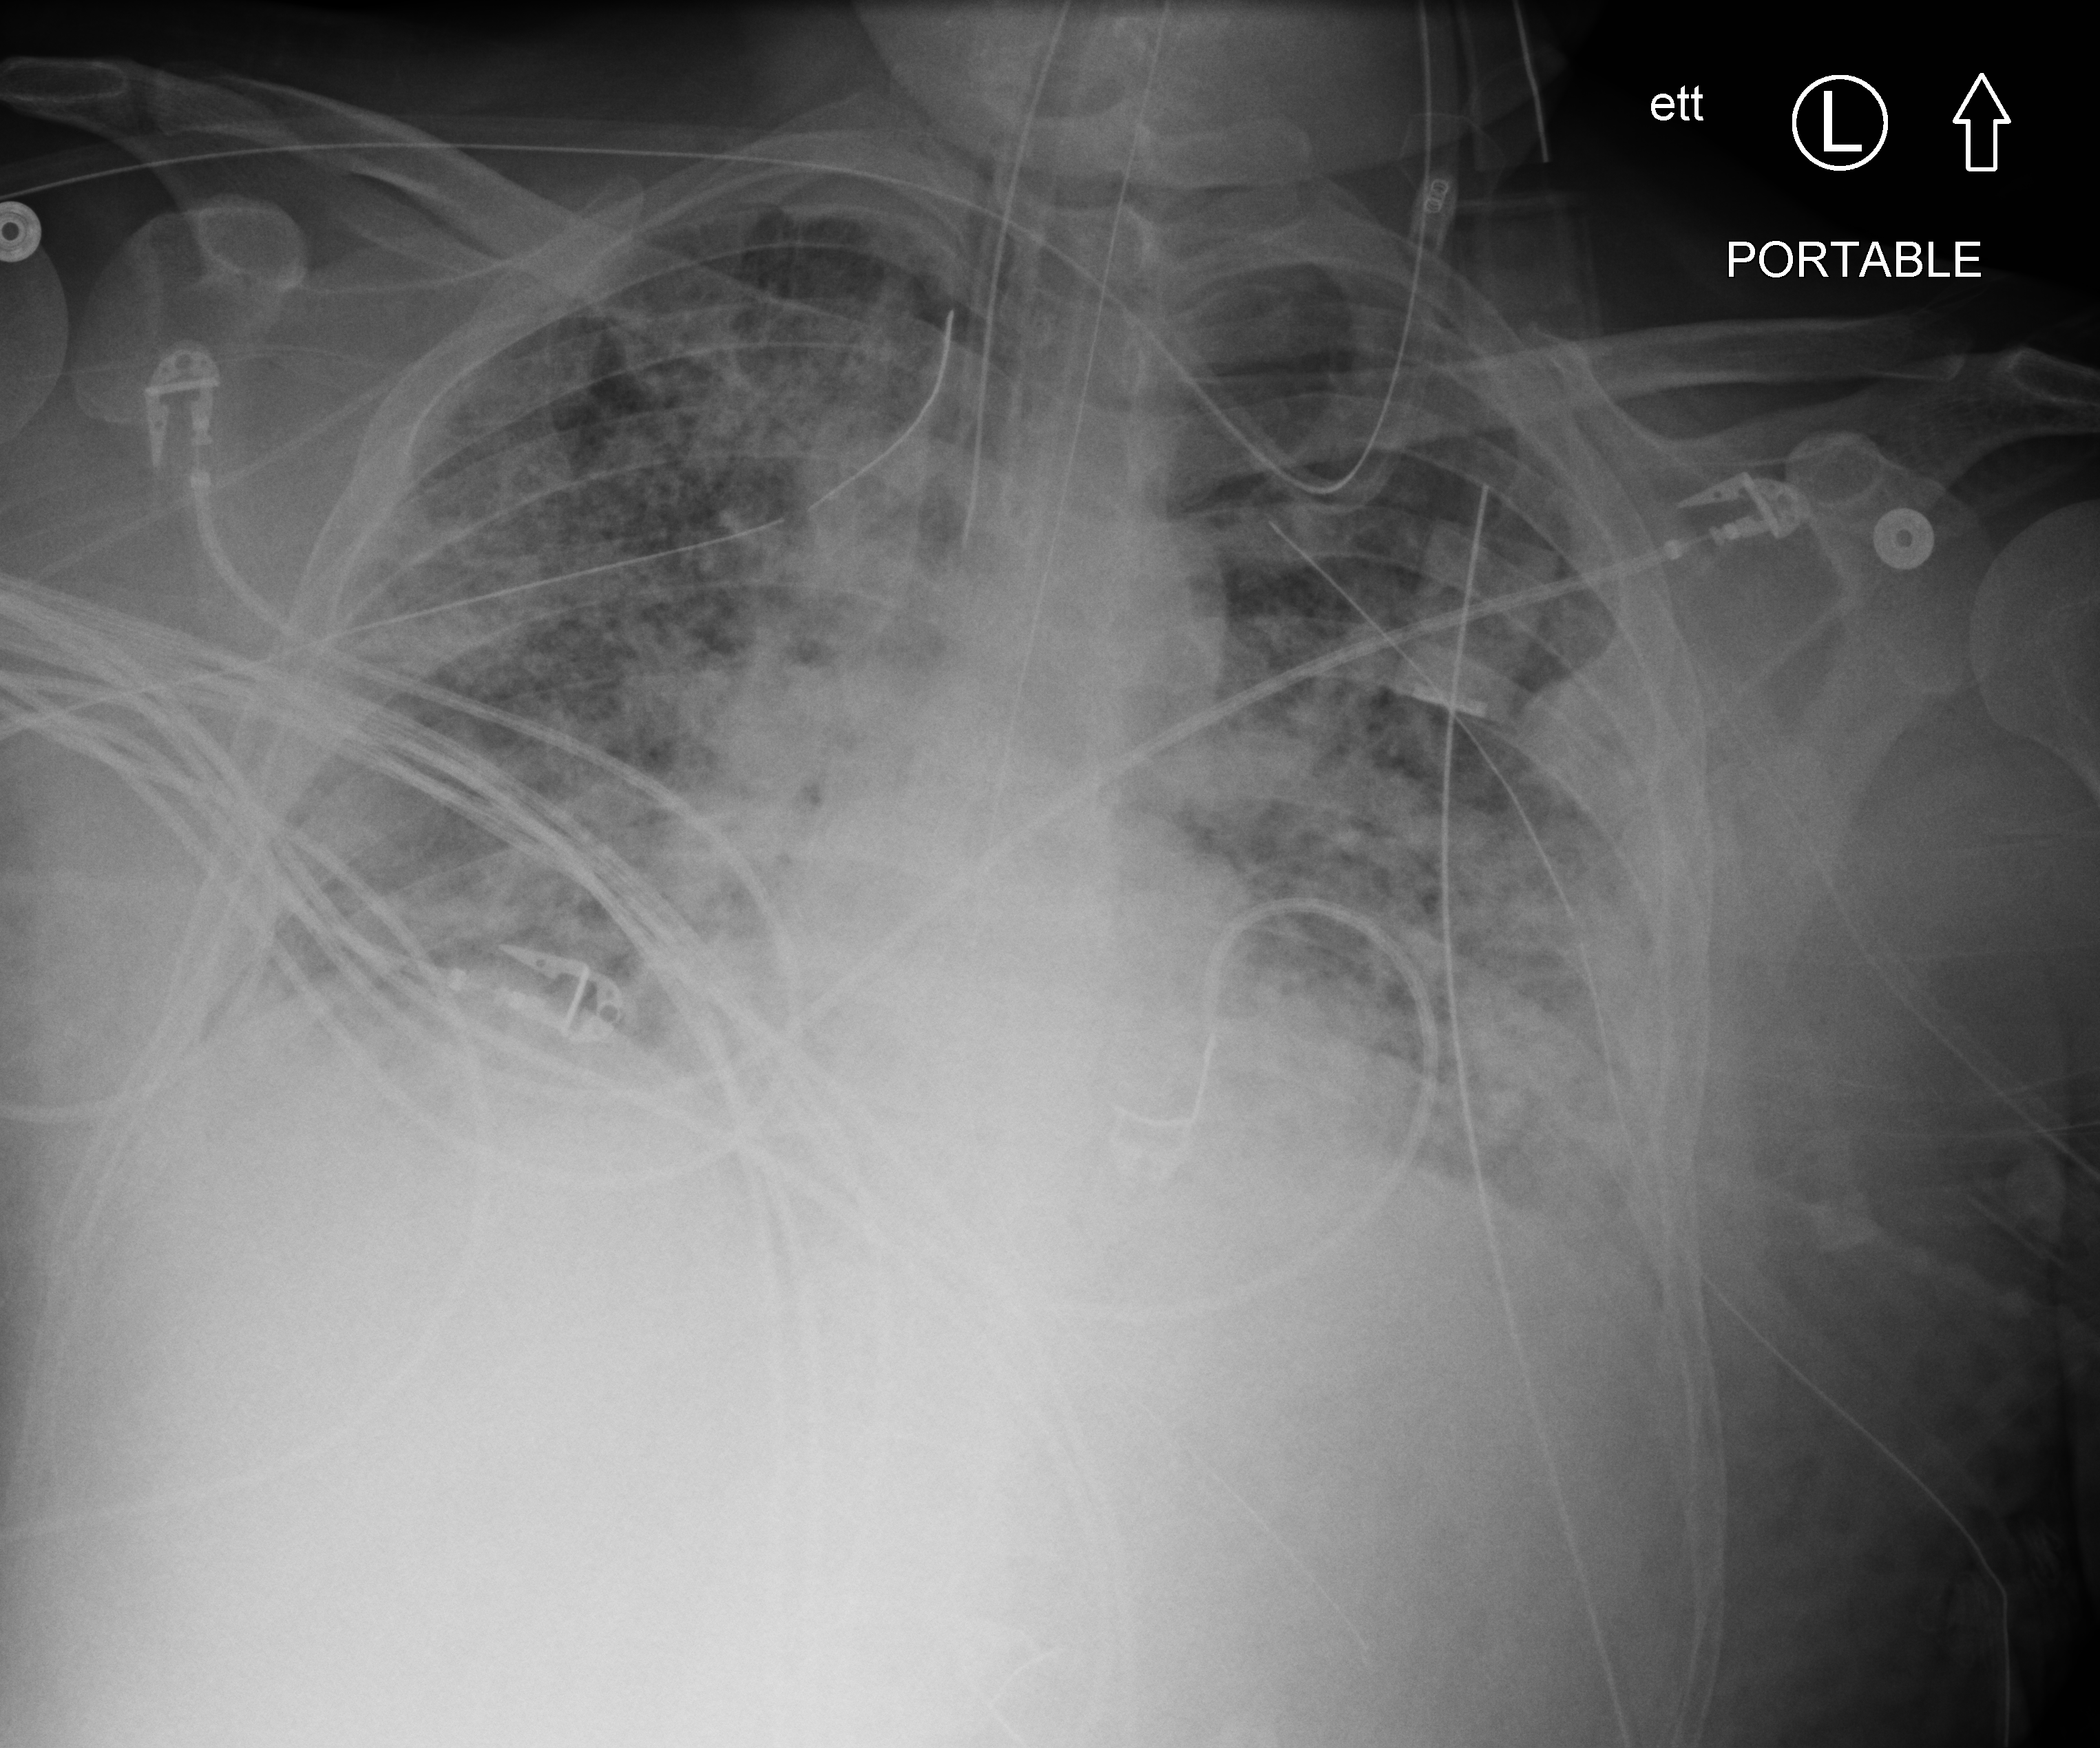
Bedside chest radiograph (computed radiography). Male patient hospitalised with COVID-19, age 18–59 years.
Hospital-stay facts (about this admission, not read from this image; timing relative to this image not recorded):
- mechanically ventilated during this hospital stay: yes
- length of hospital stay: 63 days
- COPD (admission record): no